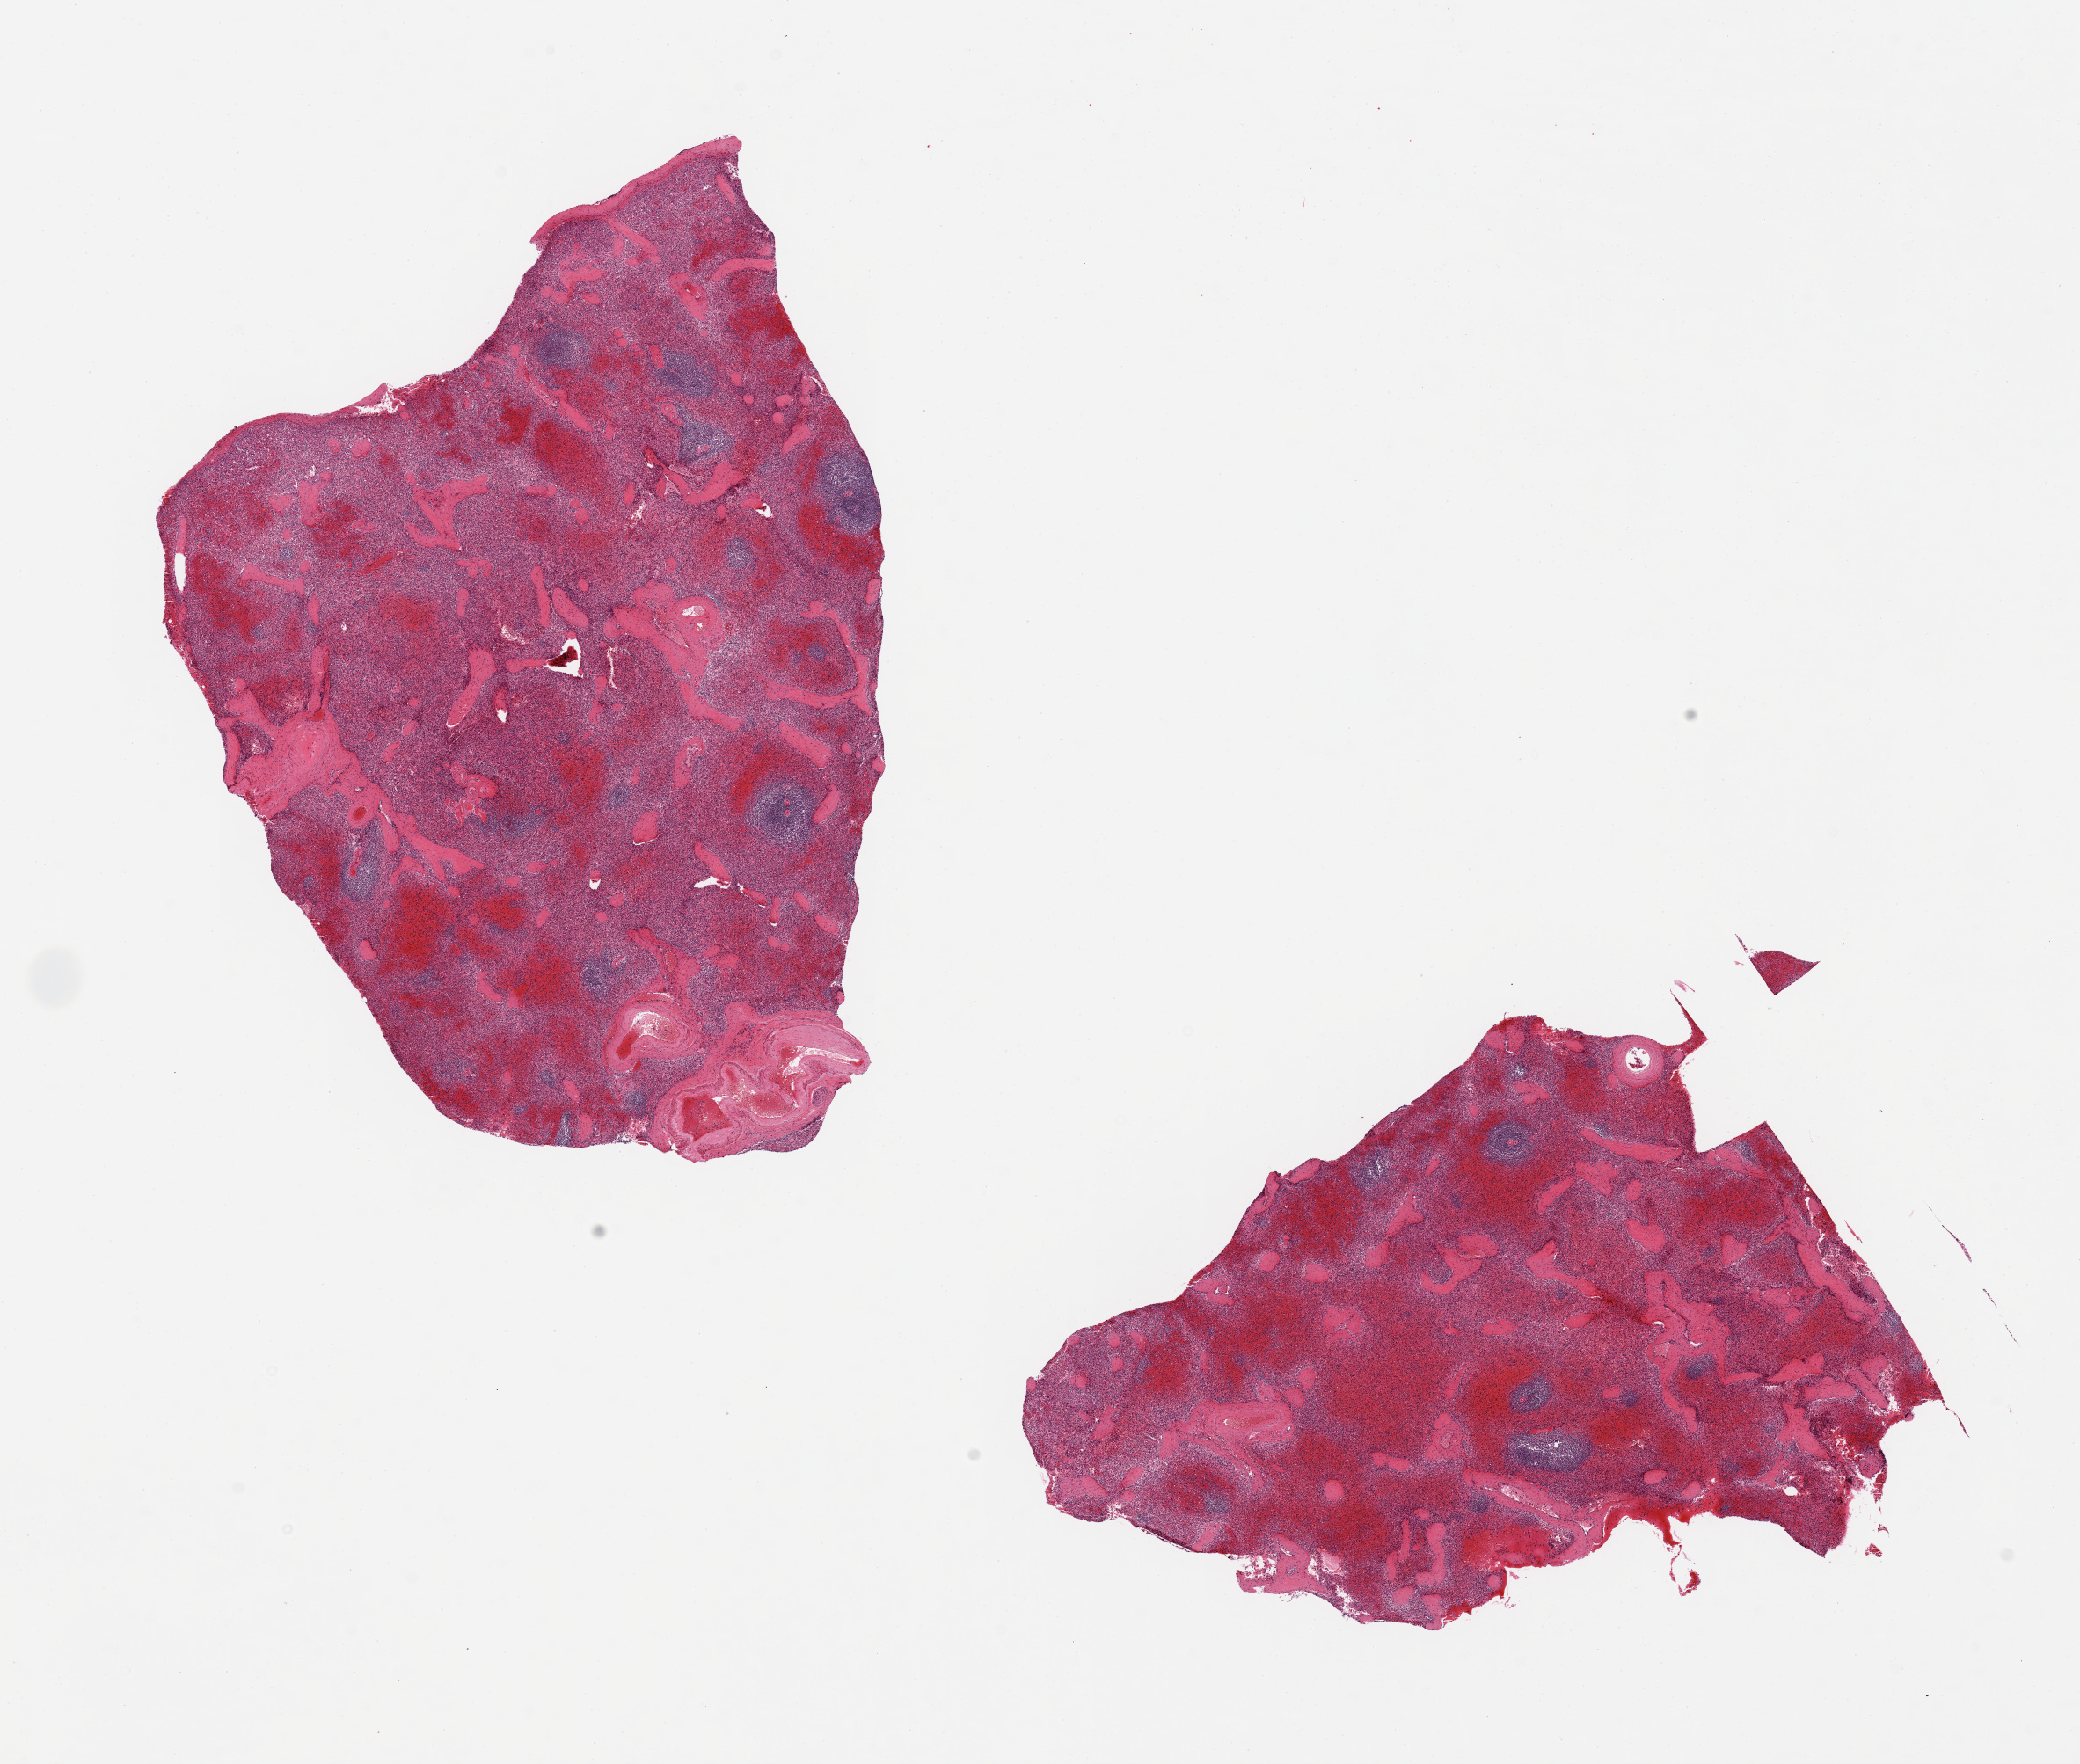
Whole-slide image, H&E stain, brightfield, whole scanned area (about 18.7 x 15.9 mm, acquisition: 20x scan) shown as a low-resolution overview. PAXgene-fixed paraffin-embedded (PFPE) section. Sampled site (target tissue): spleen. Donor tissue sample. Male donor.
Reviewer comment on this tissue sample: 2 pieces, well-preserved.